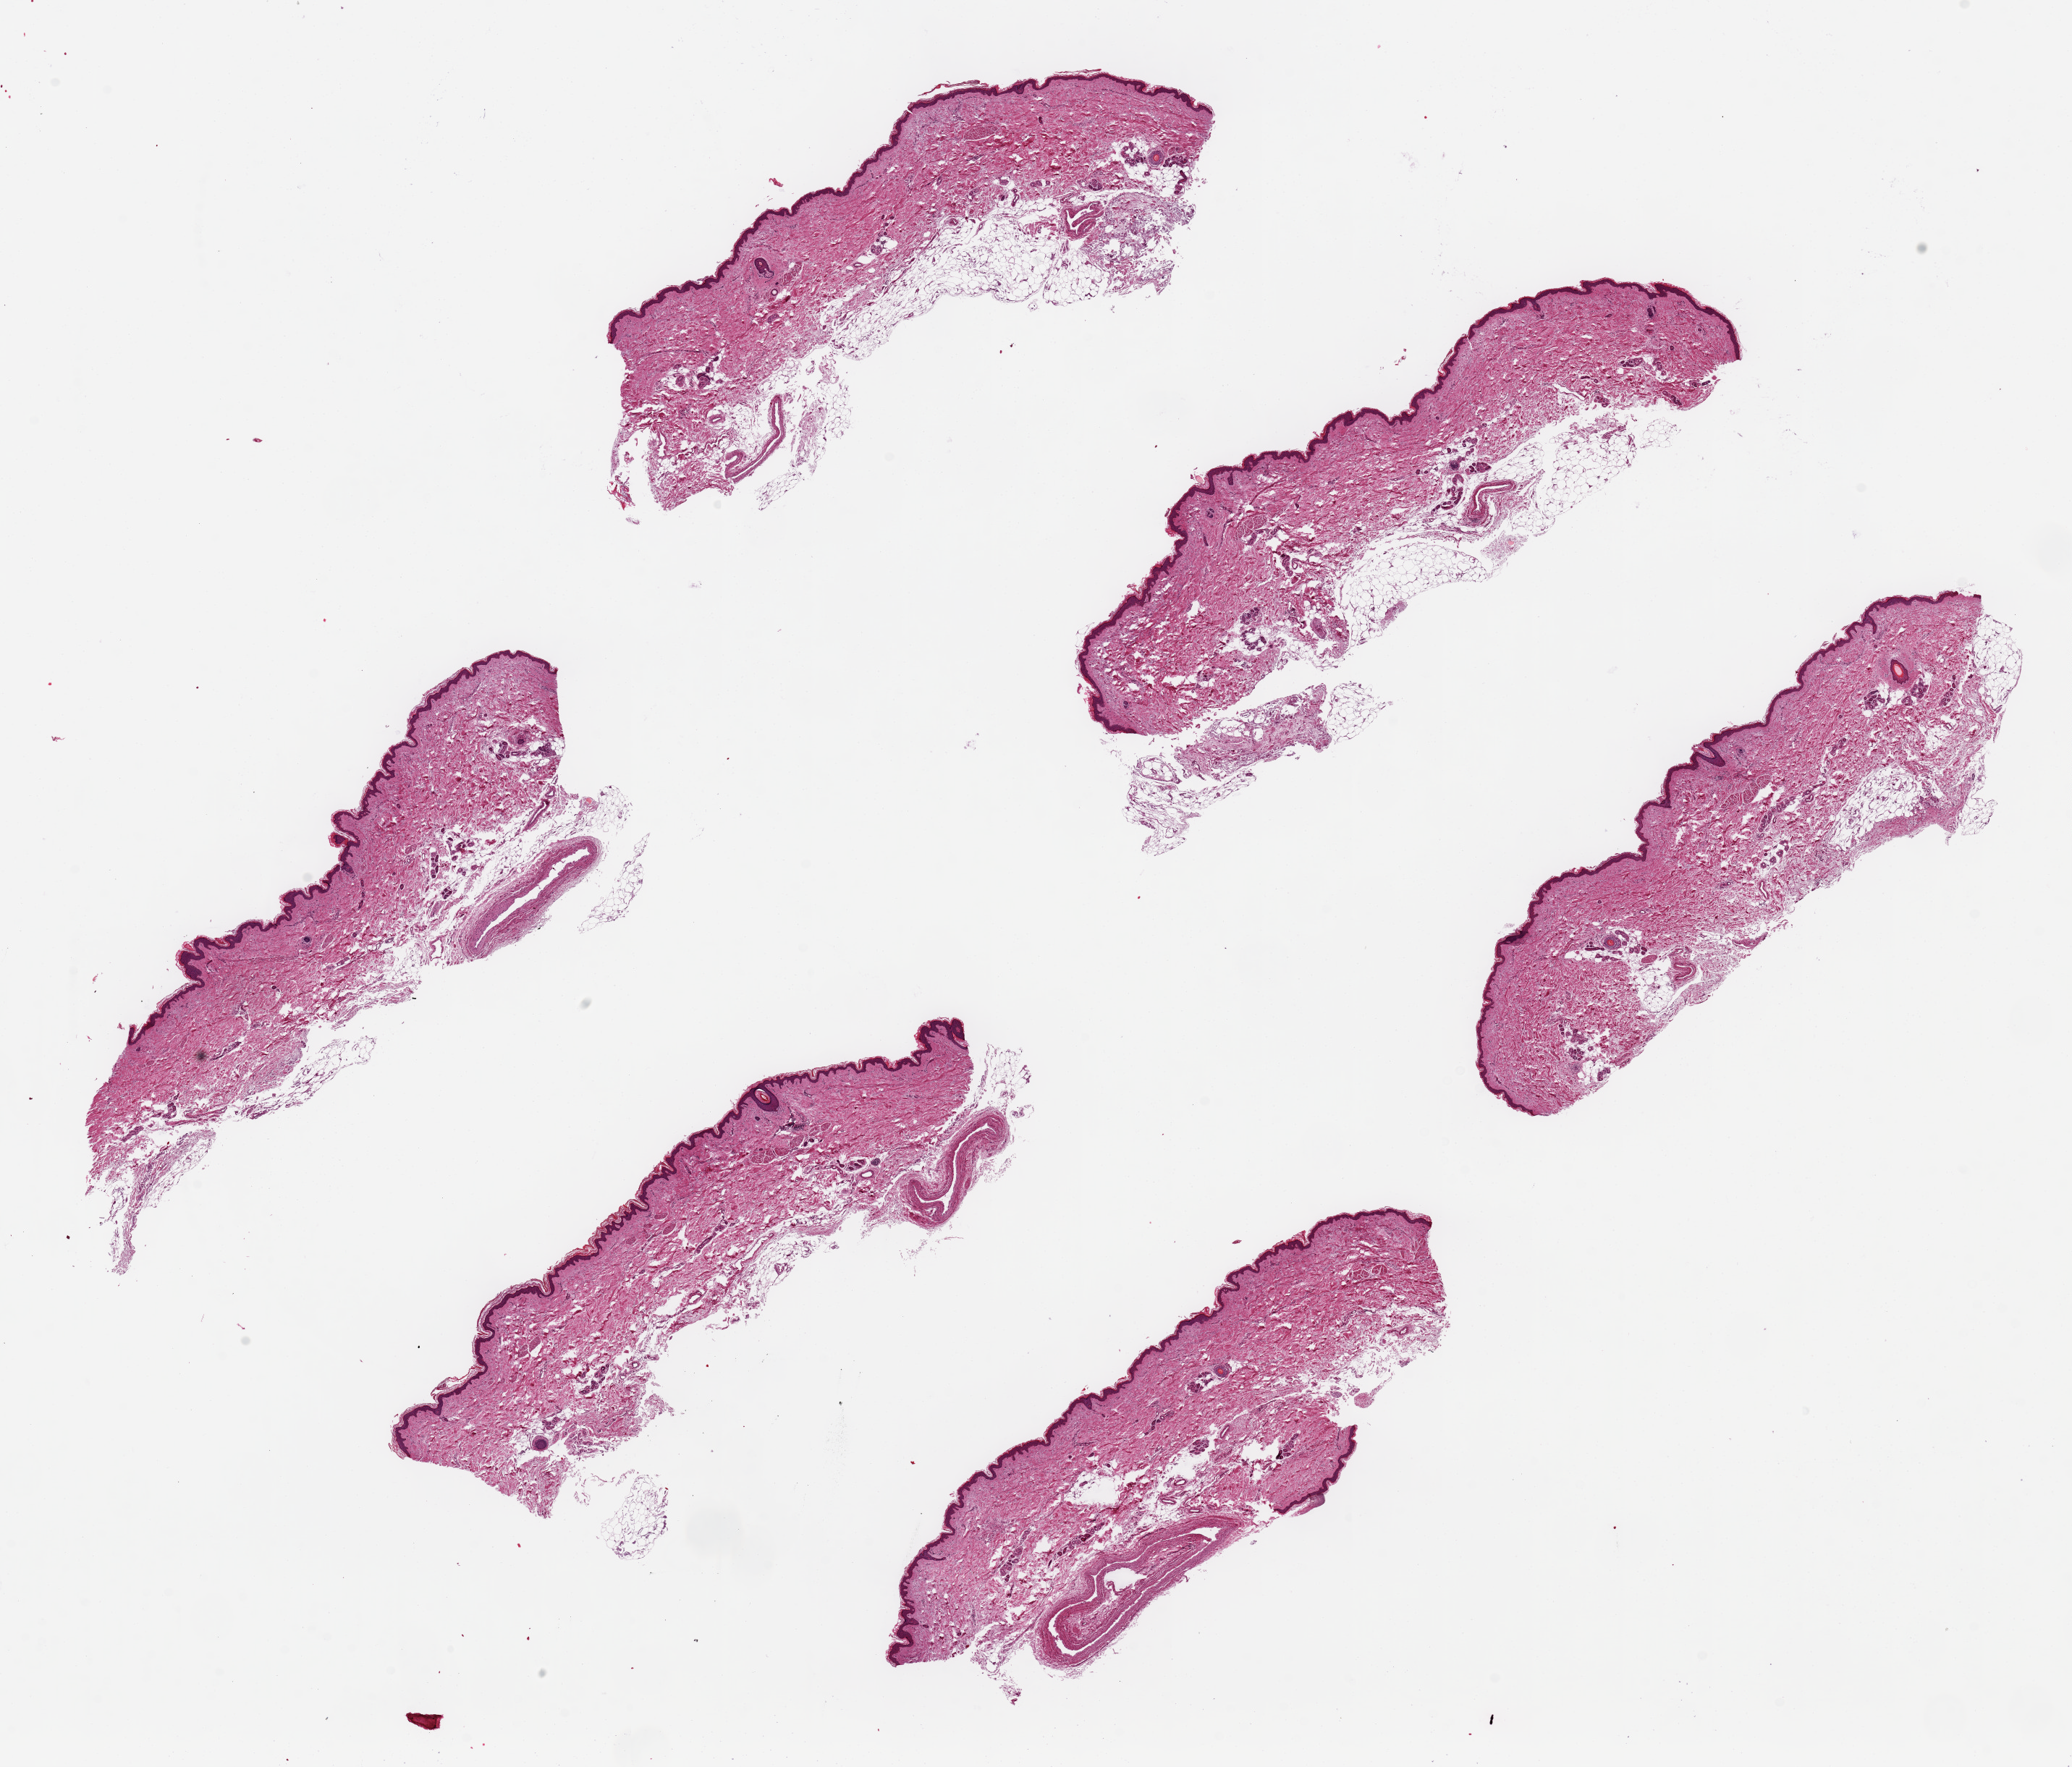
Whole-slide image, H&E stain — whole scanned area (about 22.6 x 19.3 mm, slide scanned at 20x) shown as a low-resolution overview, PAXgene-fixed paraffin-embedded (PFPE) section, target tissue: skin of lower leg, tissue donor sample. Donor sex: female.
Reviewer comment on this tissue sample: 6 pieces, up to 8x2.5 mm.